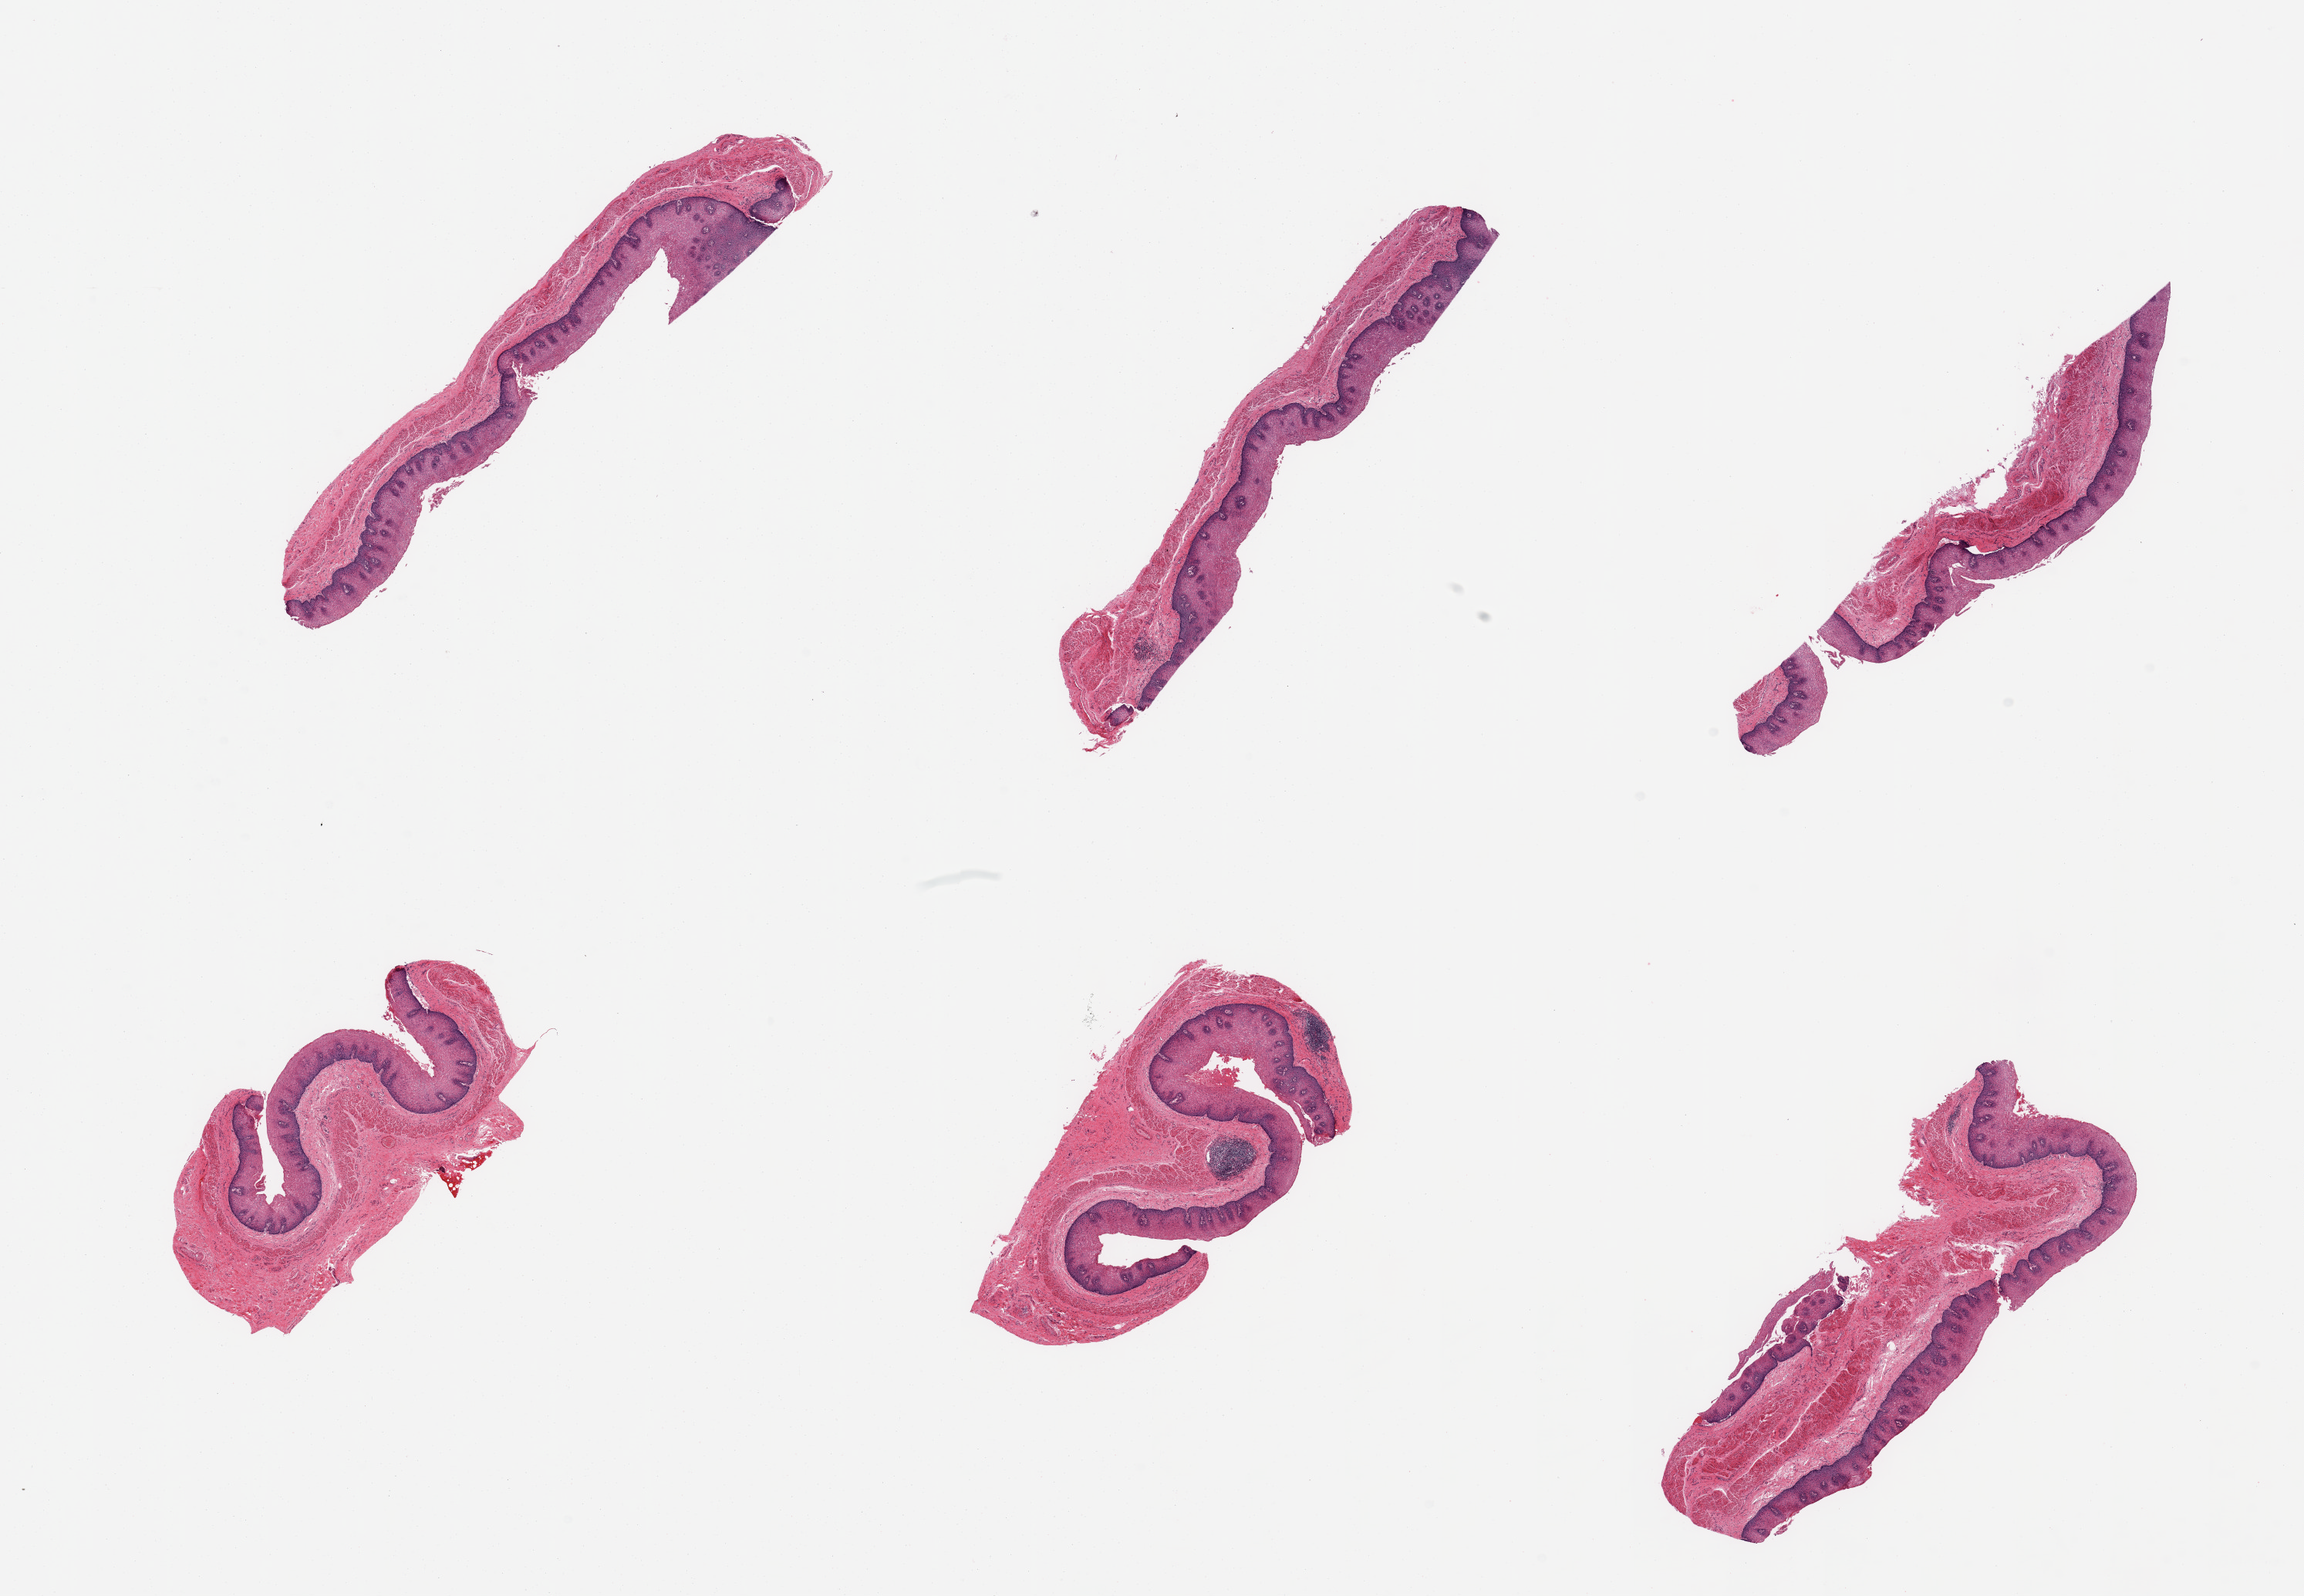
H&E whole-slide image — whole scanned area (about 23.6 x 16.4 mm, acquisition: 20x scan) shown as a low-resolution overview, PAXgene-fixed, paraffin-embedded tissue, target tissue: esophageal mucous membrane, tissue donor sample. Donor: male.
Reviewer comment on this tissue sample: 6 pieces, squamous mucosa up to ~0.4mm, 40-50% thickness.